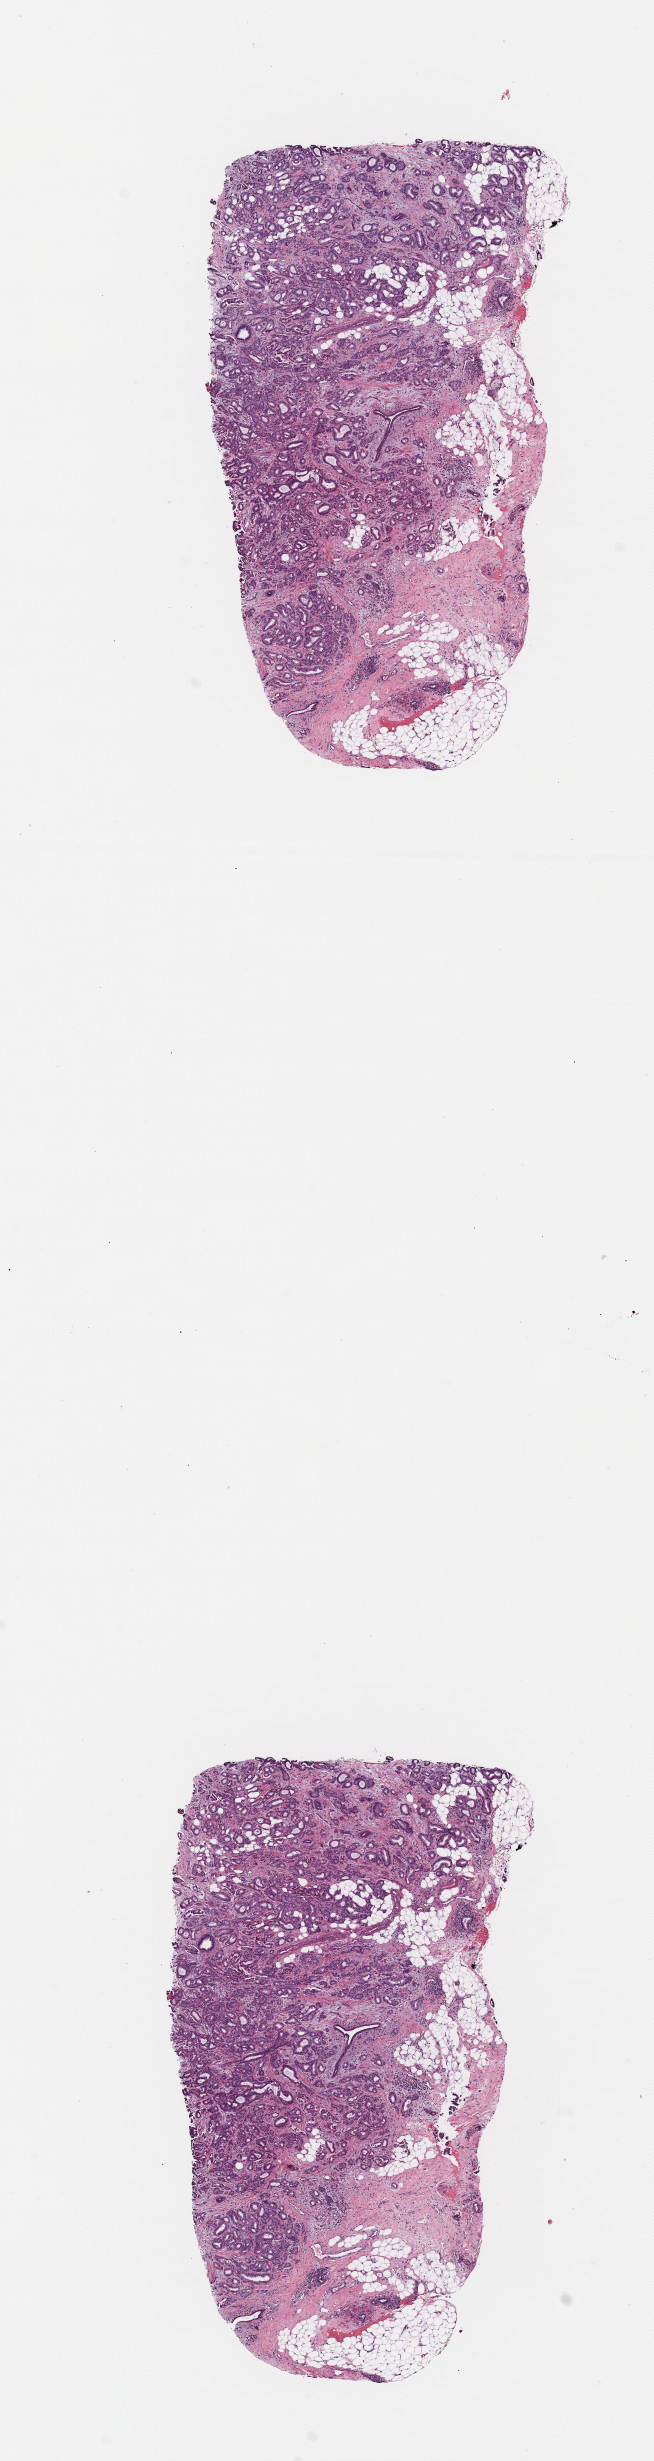
Digitized H&E-stained tissue section (whole slide) — low-resolution overview of the scanned area, about 5.1 x 19.4 mm. Formalin-fixed paraffin-embedded (FFPE) diagnostic section. Breast, primary tumour sample. Female, age 79 years at initial diagnosis.
- pathologic diagnosis: Infiltrating duct carcinoma, NOS
- lymph nodes positive (case pathology): 0 of 1 examined
- AJCC pathologic stage: IIA (7th edition)